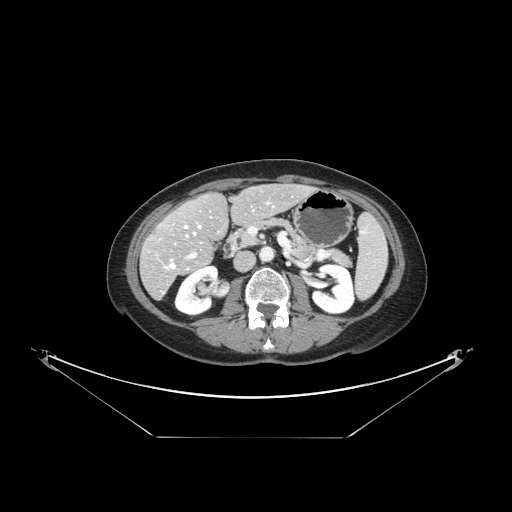
Contrast-enhanced abdominal CT, one axial slice; slice 63 of 148 in the series (ordered by position); 120 kVp; soft-tissue window (W 400 / L 40 HU); 2.5 mm slice thickness; 512 × 512 image matrix, field of view 500 × 500 mm. Female patient, age 73 years. Case-level facts recorded for this patient, not image findings: diagnosis: colorectal cancer liver metastases, imaged before liver resection; multiple liver metastases: no; largest metastasis: 1 cm; disease in both lobes: no.
Structures marked on this image (outlined manually by an expert reader):
- hepatic veins: bounding box (x1, y1, x2, y2) in pixels: (165, 203, 274, 269)
- liver: (142, 185, 312, 298)
- planned liver remnant (the part of the liver to remain after resection): (166, 185, 311, 250)
- portal vein (with intrahepatic branches): (190, 253, 196, 257)